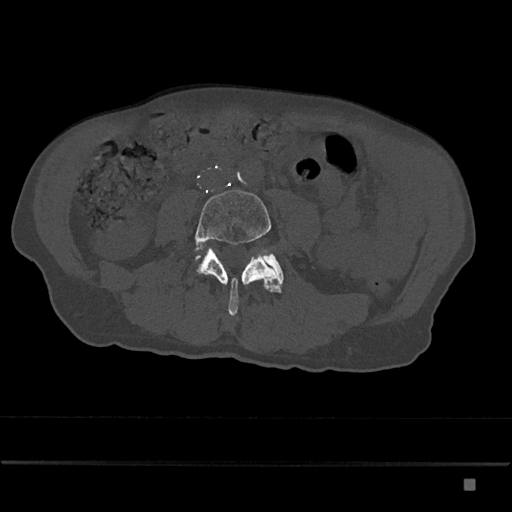
CT including the spine, one axial slice. Slice 329 of 797 in the series (ordered by position). Reconstruction kernel Br40s/3. Bone window (W 1800 / L 400 HU). 0.5 mm slice thickness. 512 × 512 image matrix. Male patient, age 72 years. From the clinical record (not read from this slice): primary cancer: prostate.
Annotated regions visible in this slice (semi-automatically segmented with operator editing):
- L4 vertebra: bounding box <195,190,282,316> (left, top, right, bottom; pixels)
- L5 vertebra: <196,254,283,292>